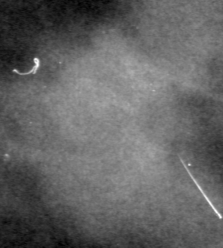
Region of interest cut from a scanned film mammogram (one marked finding), right breast, MLO view.
- Marked abnormality: mass, shape lobulated, margins ill defined; BI-RADS assessment category 4; pathology (as recorded): malignant.